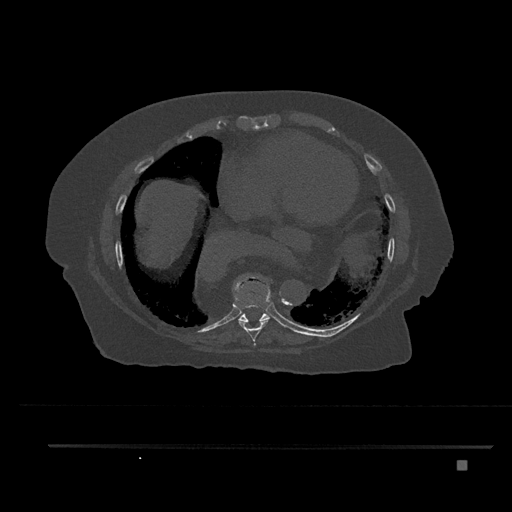
CT including the spine, one axial slice; slice 423 of 797 in the series (ordered by position); reconstruction kernel Br40s/3; bone window (W 1800 / L 400 HU); 0.5 mm slice thickness; 512 × 512 image matrix, field of view 437 × 437 mm. Patient: female, 76 years. Case-level facts recorded for this patient, not image findings: primary cancer: lung.
Outlined on this slice (semi-automatic segmentation, software-assisted and operator-edited):
- T8 vertebra: box from (x=232, y=276) to (x=271, y=347) px
- T9 vertebra: (x=226, y=275)–(x=271, y=324)